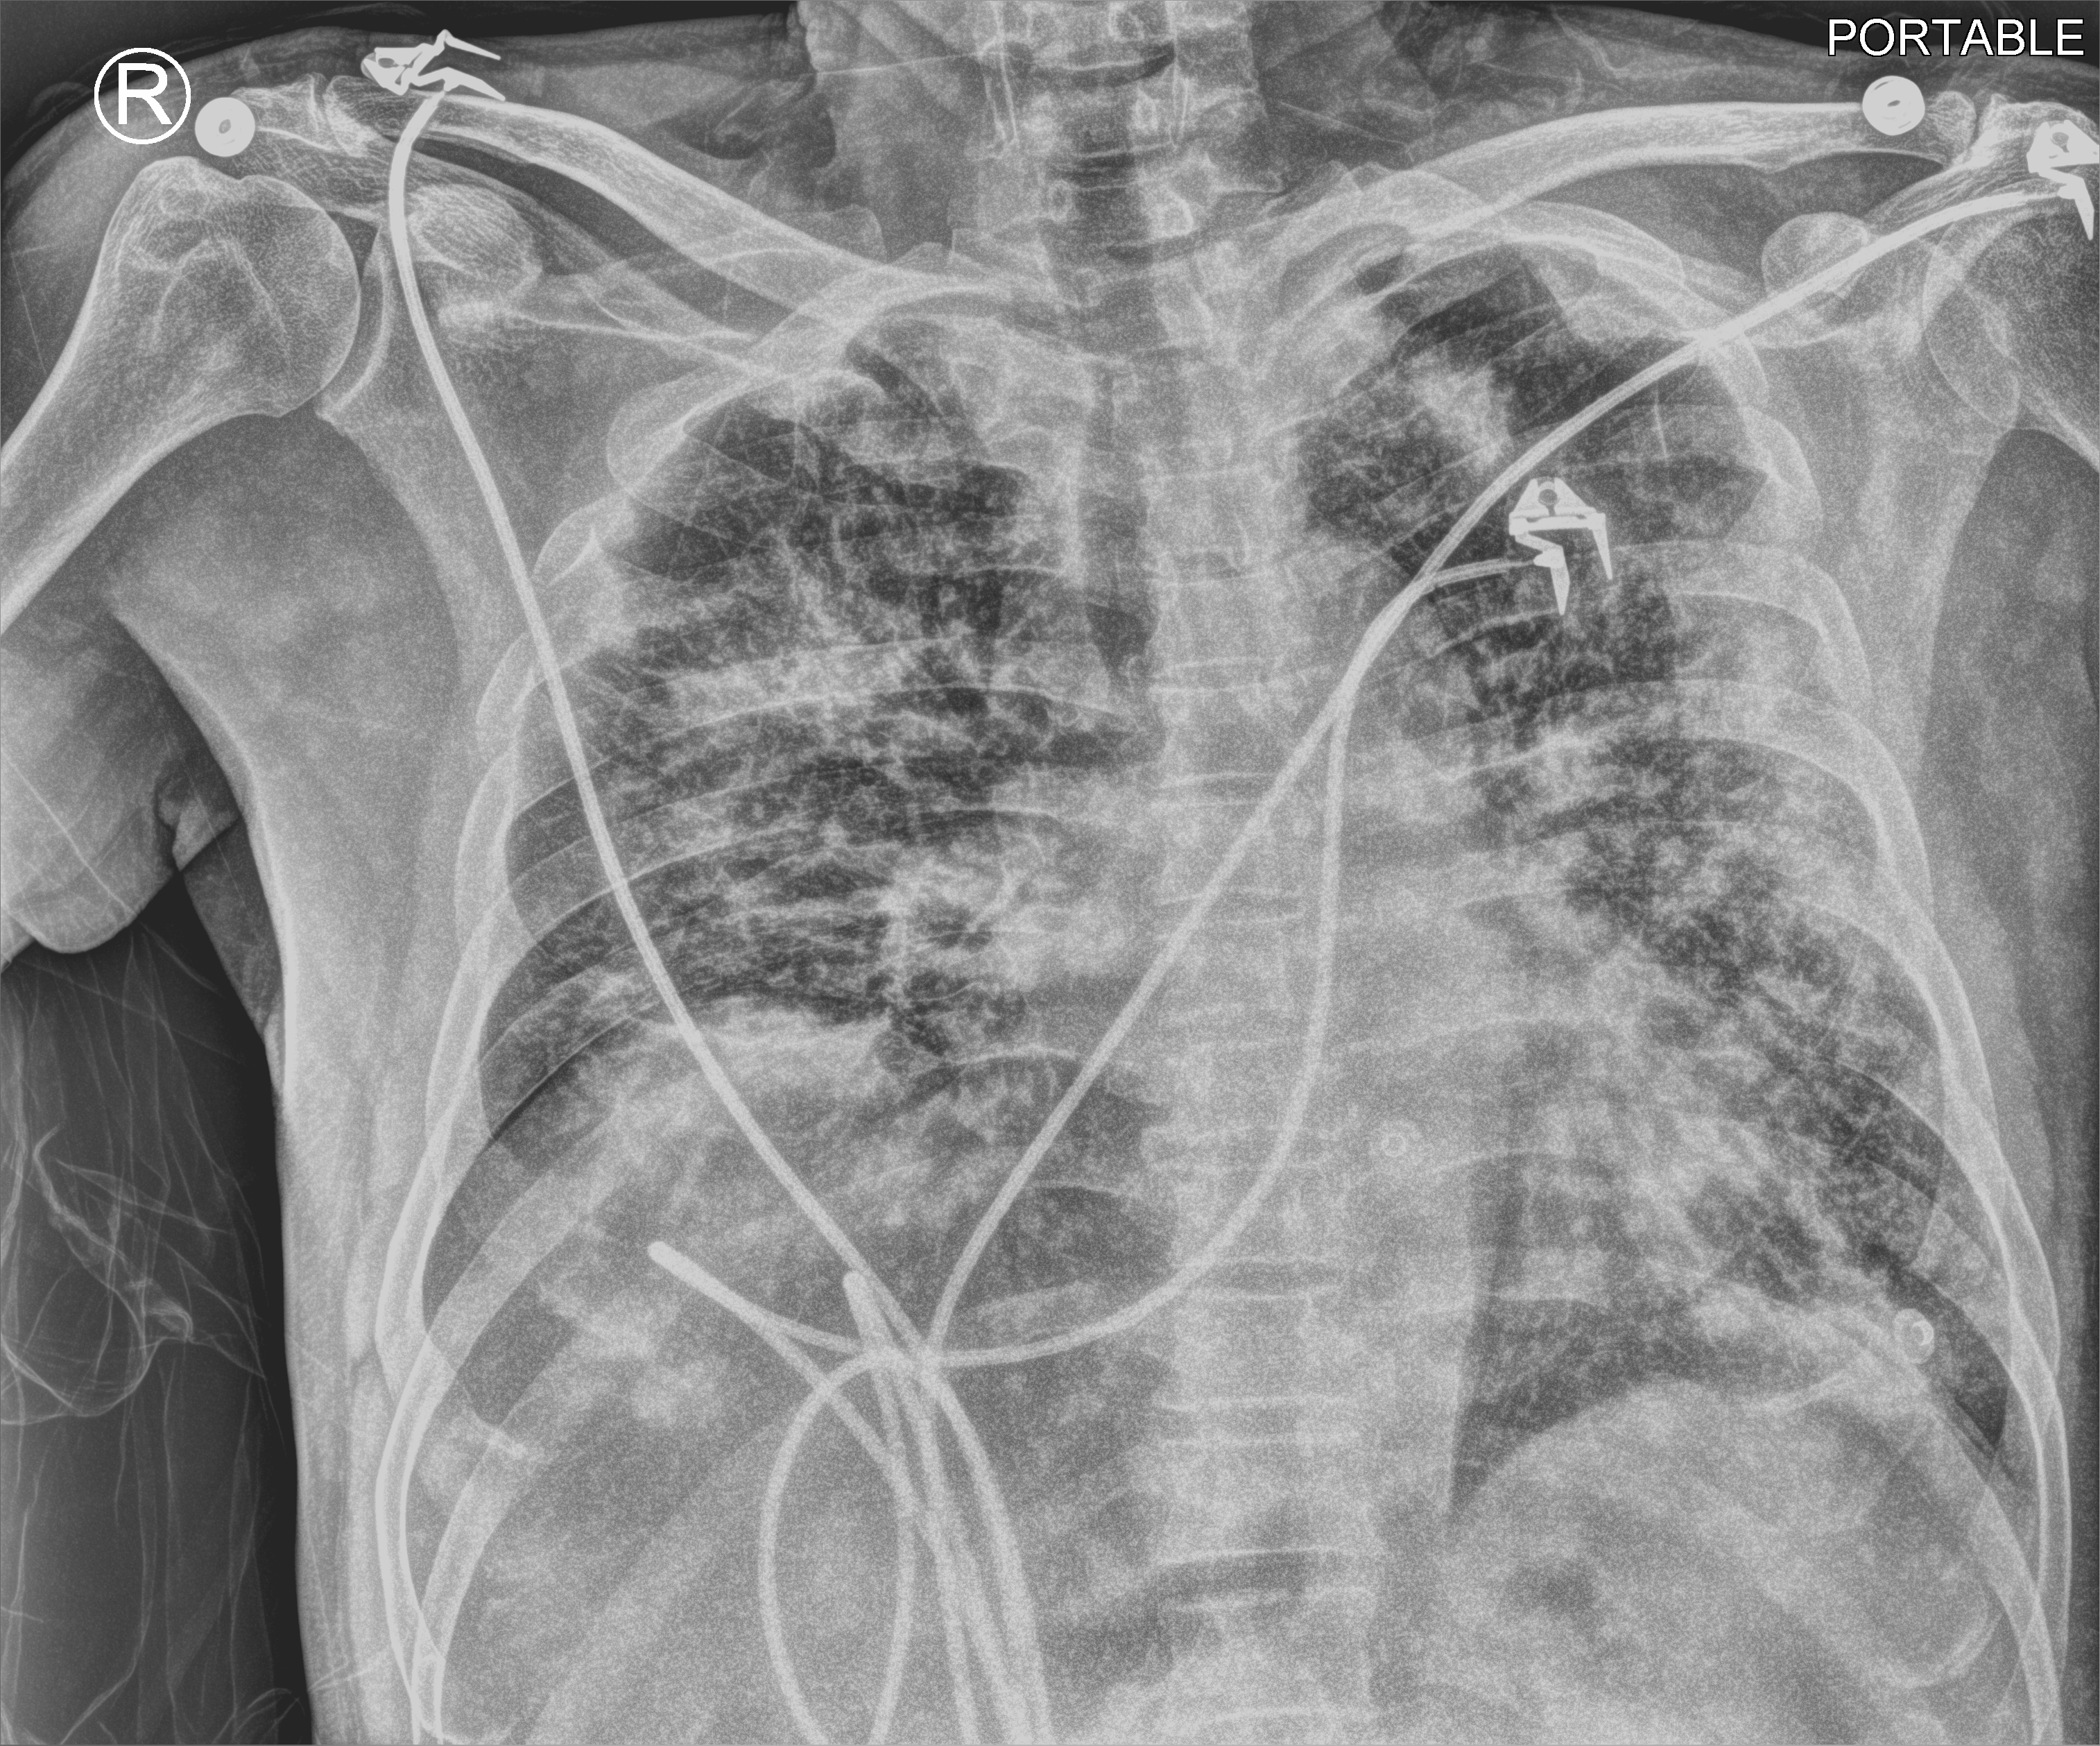
Portable chest radiograph; anteroposterior (AP) projection. Male patient hospitalised with COVID-19, age 60–74 years.
From the hospital-stay record, not from the radiograph (when in the stay this image was taken is not recorded): mechanically ventilated during this hospital stay: no; admitted to intensive care during this hospital stay: no; chronic kidney disease (admission record): no.